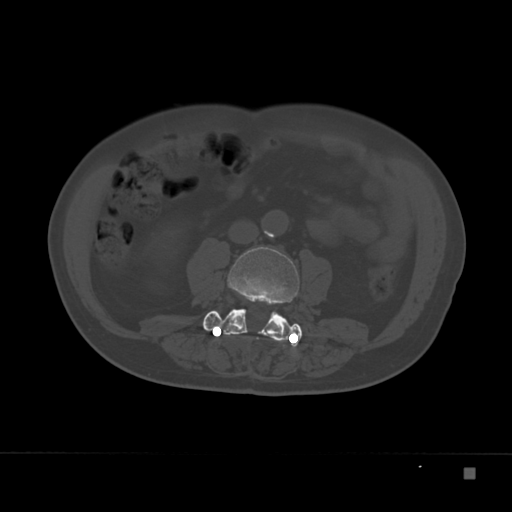
CT including the spine, one axial slice; reconstruction kernel Br40s; 120 kVp; bone window (W 1800 / L 400 HU); 512 × 512 image matrix, field of view 389 × 389 mm. Male patient, age 72 years. From the clinical record (not read from this slice): primary cancer: skeletal.
Annotated regions visible in this slice (semi-automatically segmented with operator editing):
- L3 vertebra: bounding box <204,247,302,340> (left, top, right, bottom; pixels)
- L4 vertebra: <203,311,302,345>